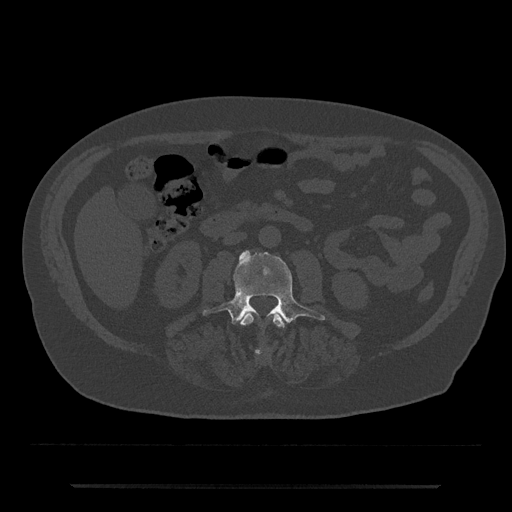
CT including the spine, one axial slice. Slice 424 of 797 in the series (ordered by position). Bone window (W 1800 / L 400 HU). 0.5 mm slice thickness. 512 × 512 image matrix, field of view 434 × 434 mm. Male patient, age 80 years. From the clinical record (not read from this slice): primary cancer: prostate; vertebrae with lytic lesions (as recorded): L1, T11.
Outlined on this slice (semi-automatic segmentation, software-assisted and operator-edited):
- L2 vertebra: box from (x=241, y=312) to (x=285, y=354) px
- L3 vertebra: (x=202, y=251)–(x=325, y=324)